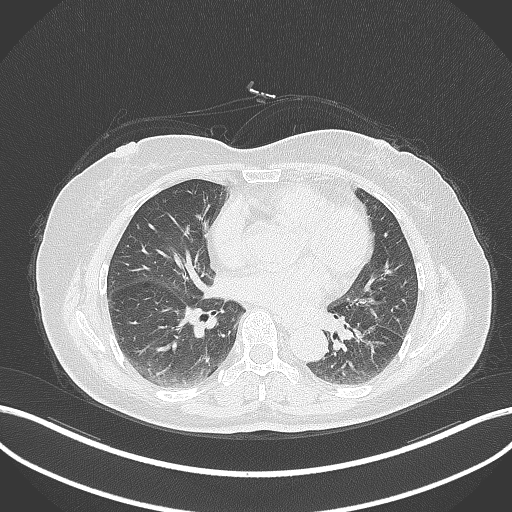
Chest CT, one axial slice; reconstruction kernel B70f; 120 kVp; lung window (W 1500 / L -600 HU); 512 × 512 image matrix, field of view 400 × 400 mm. Female patient, age 59 years. Case-level facts recorded for this patient, not image findings: clinical TNM (as recorded): T2a N0 M0; histopathological grade: G2-3.
Annotated regions visible in this slice (rectangle marked by the reading radiologist):
- lung tumour (recorded histology: adenocarcinoma): bounding box (x1, y1, x2, y2) in pixels: (348, 321, 388, 371)